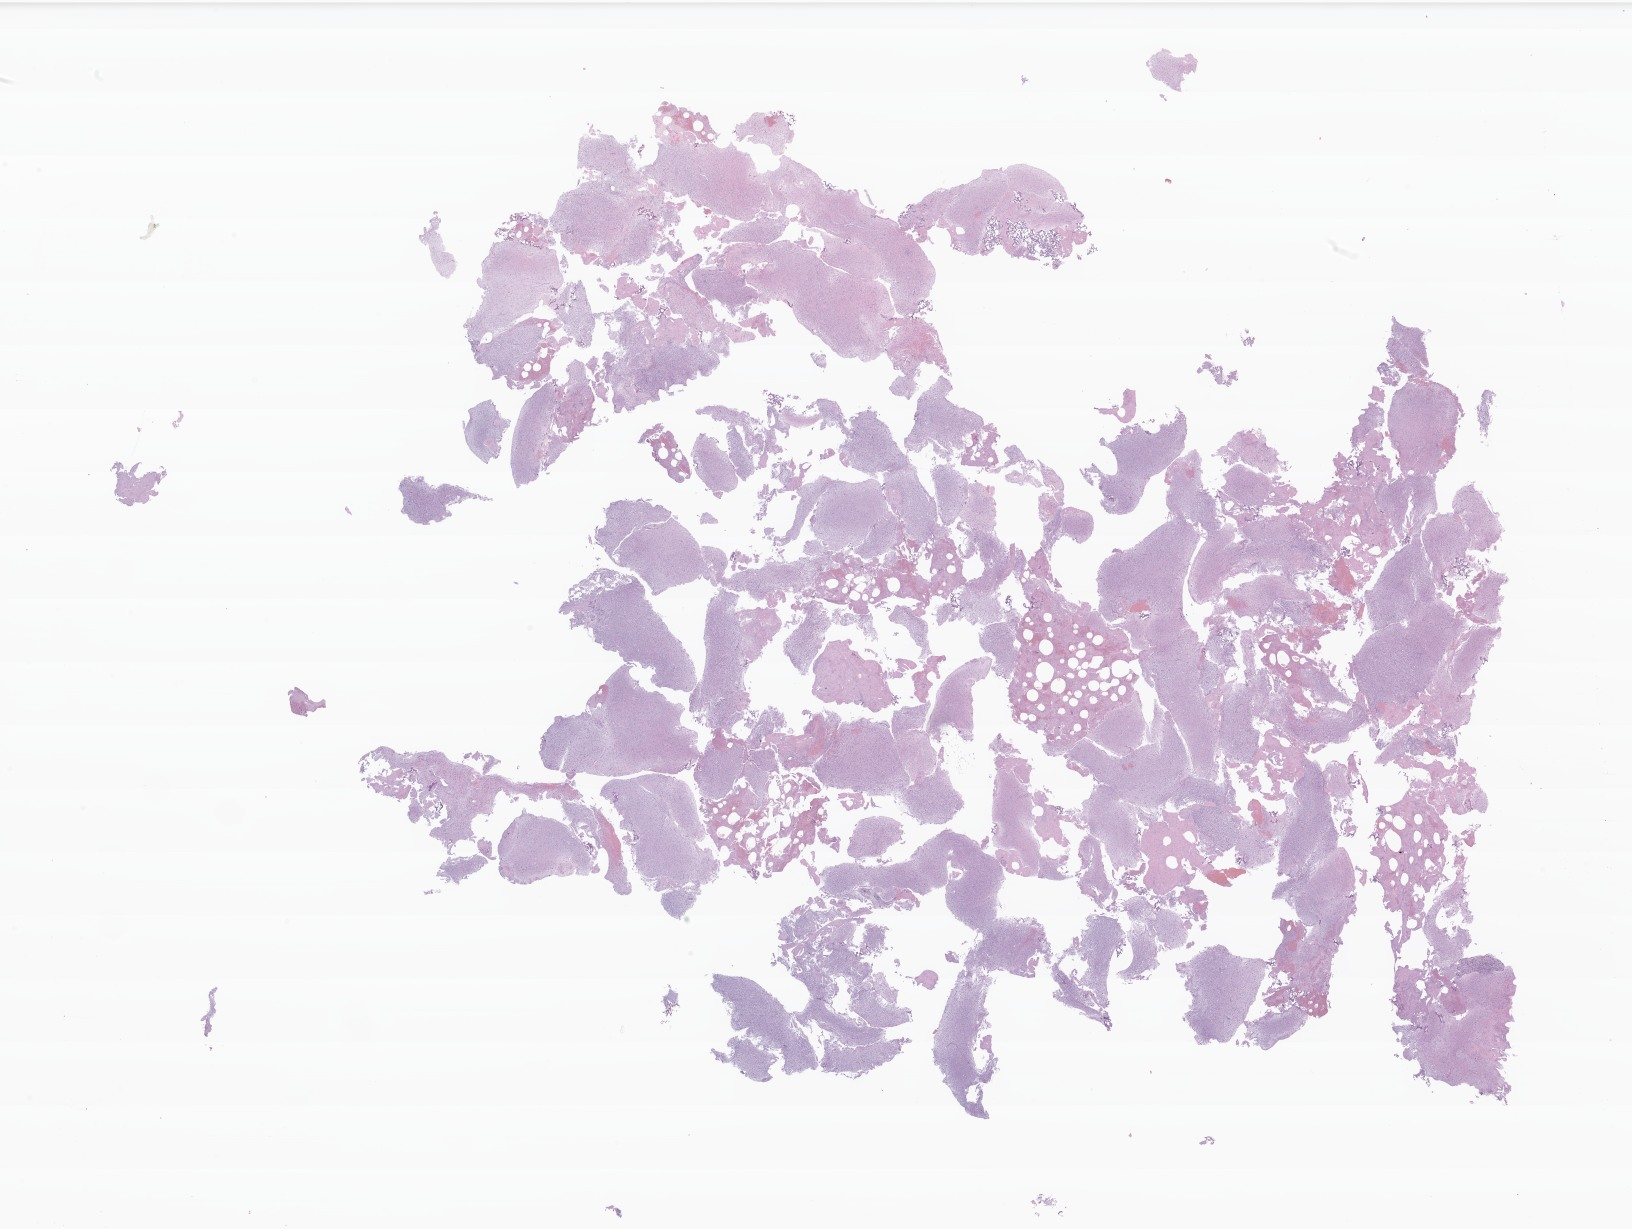
Whole-slide image, H&E stain of tumor tissue from the cerebellum, low-resolution overview of the scanned area, about 27.5 x 20.7 mm; formalin-fixed paraffin-embedded section. Female patient, age 195 months (16 years 3 months).
• diagnosis: Pilocytic astrocytoma